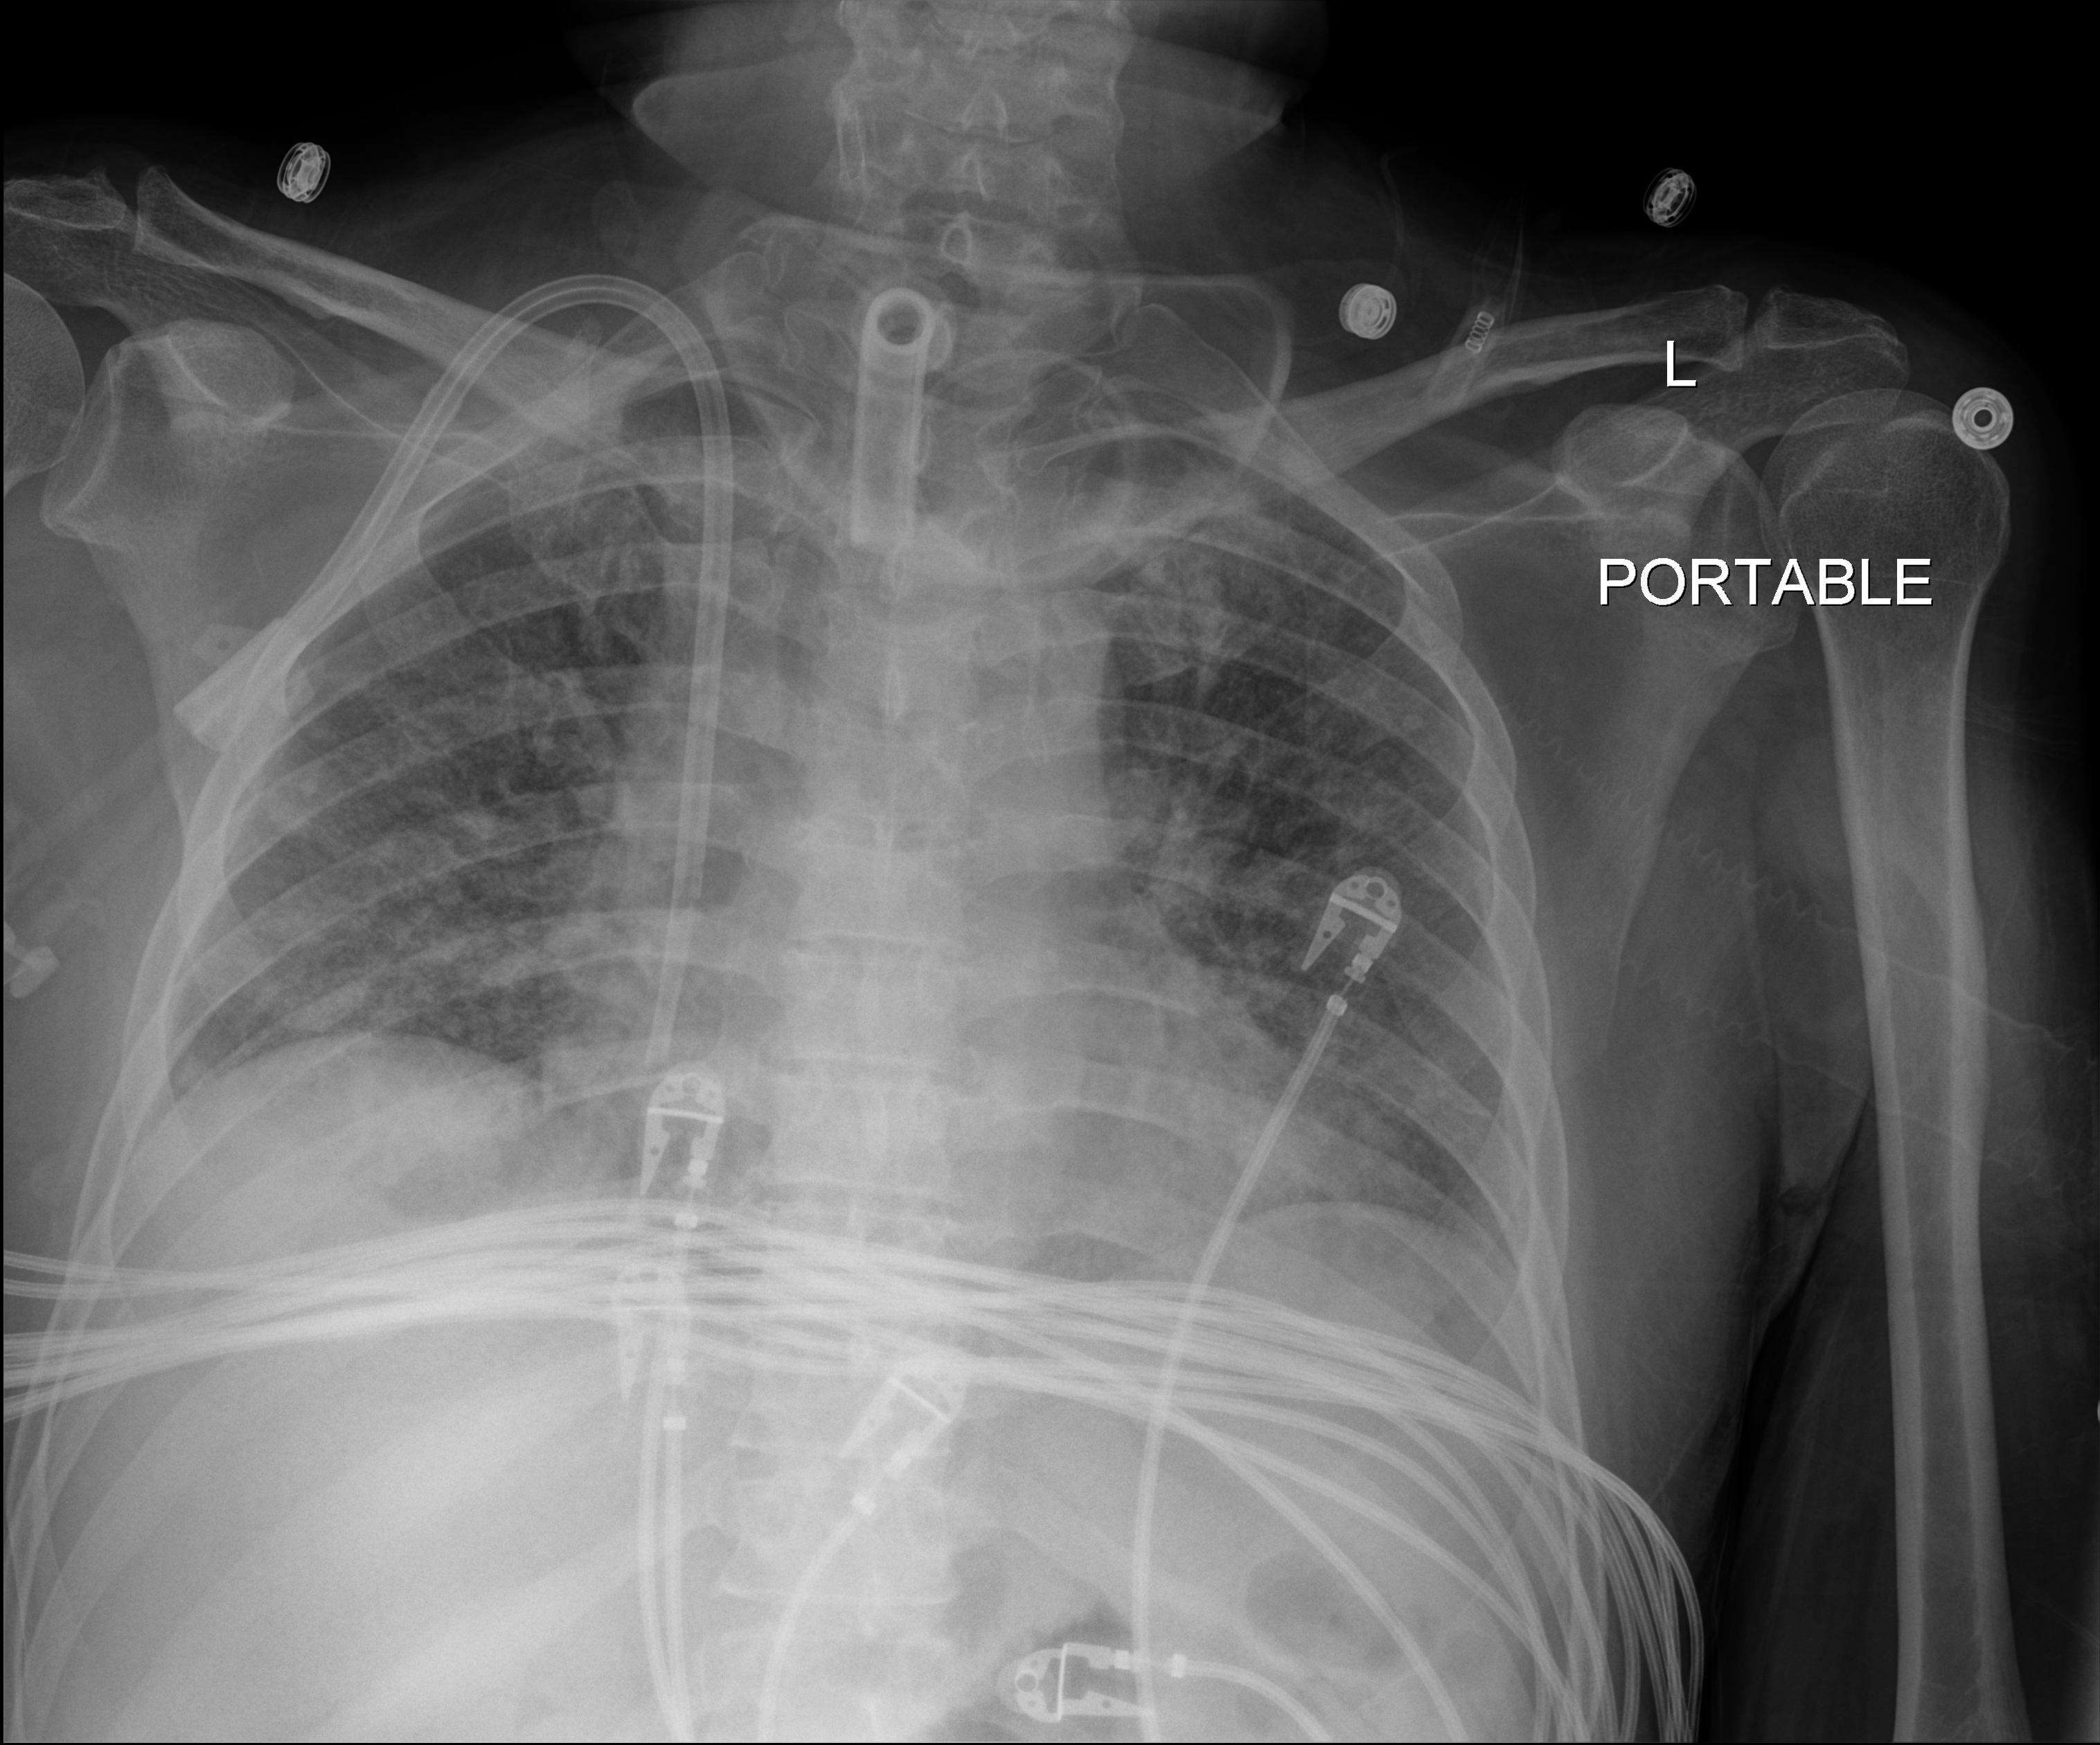
Bedside chest radiograph (digital radiography); anteroposterior (AP) projection. Patient hospitalised with COVID-19; male, aged 18–59 years.
Admission-level facts for this patient (not findings on this image; timing relative to this image not recorded): mechanically ventilated during this hospital stay: yes.